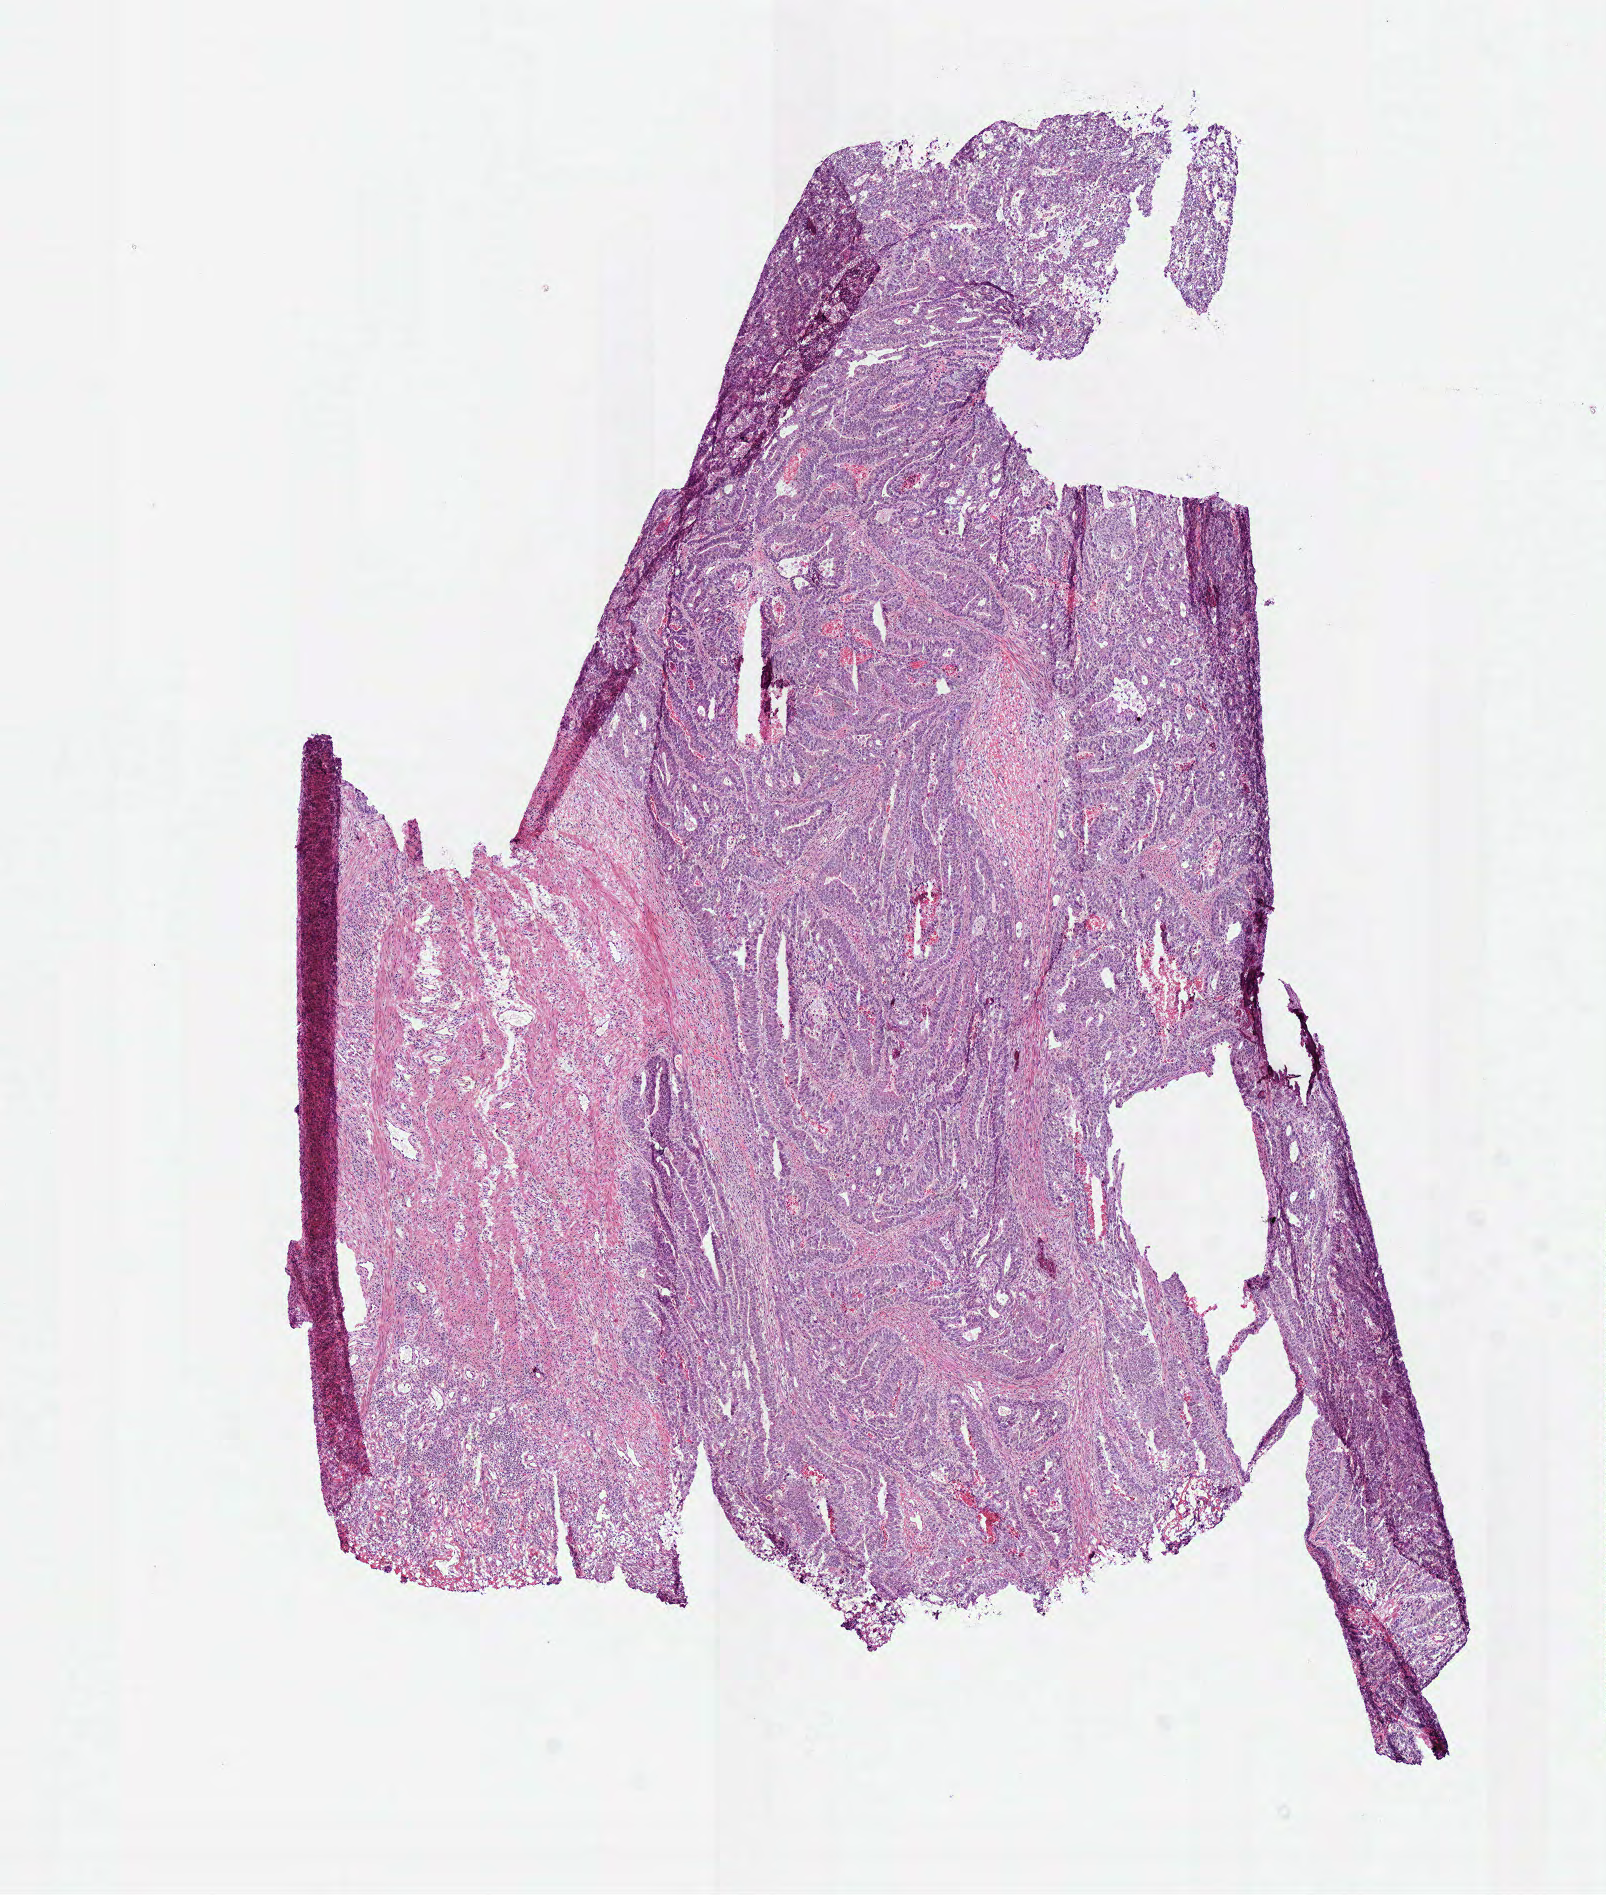
Digitized H&E tissue section (whole slide) — low-resolution overview of the scanned area, about 6.3 x 7.5 mm; frozen section from the bottom of the tissue portion; primary tumour sample from the rectum. Female patient; age at initial diagnosis 57 years. Slide review estimates, as recorded: tumour cells 65%, tumour nuclei 75%, normal cells 0%, stromal cells 30%, necrosis 5%.
• AJCC pathologic stage: IV (7th edition)
• diagnosis: Tubular adenocarcinoma
• lymph nodes positive (case pathology): 2 of 13 examined
• TNM: T3 N1b M1